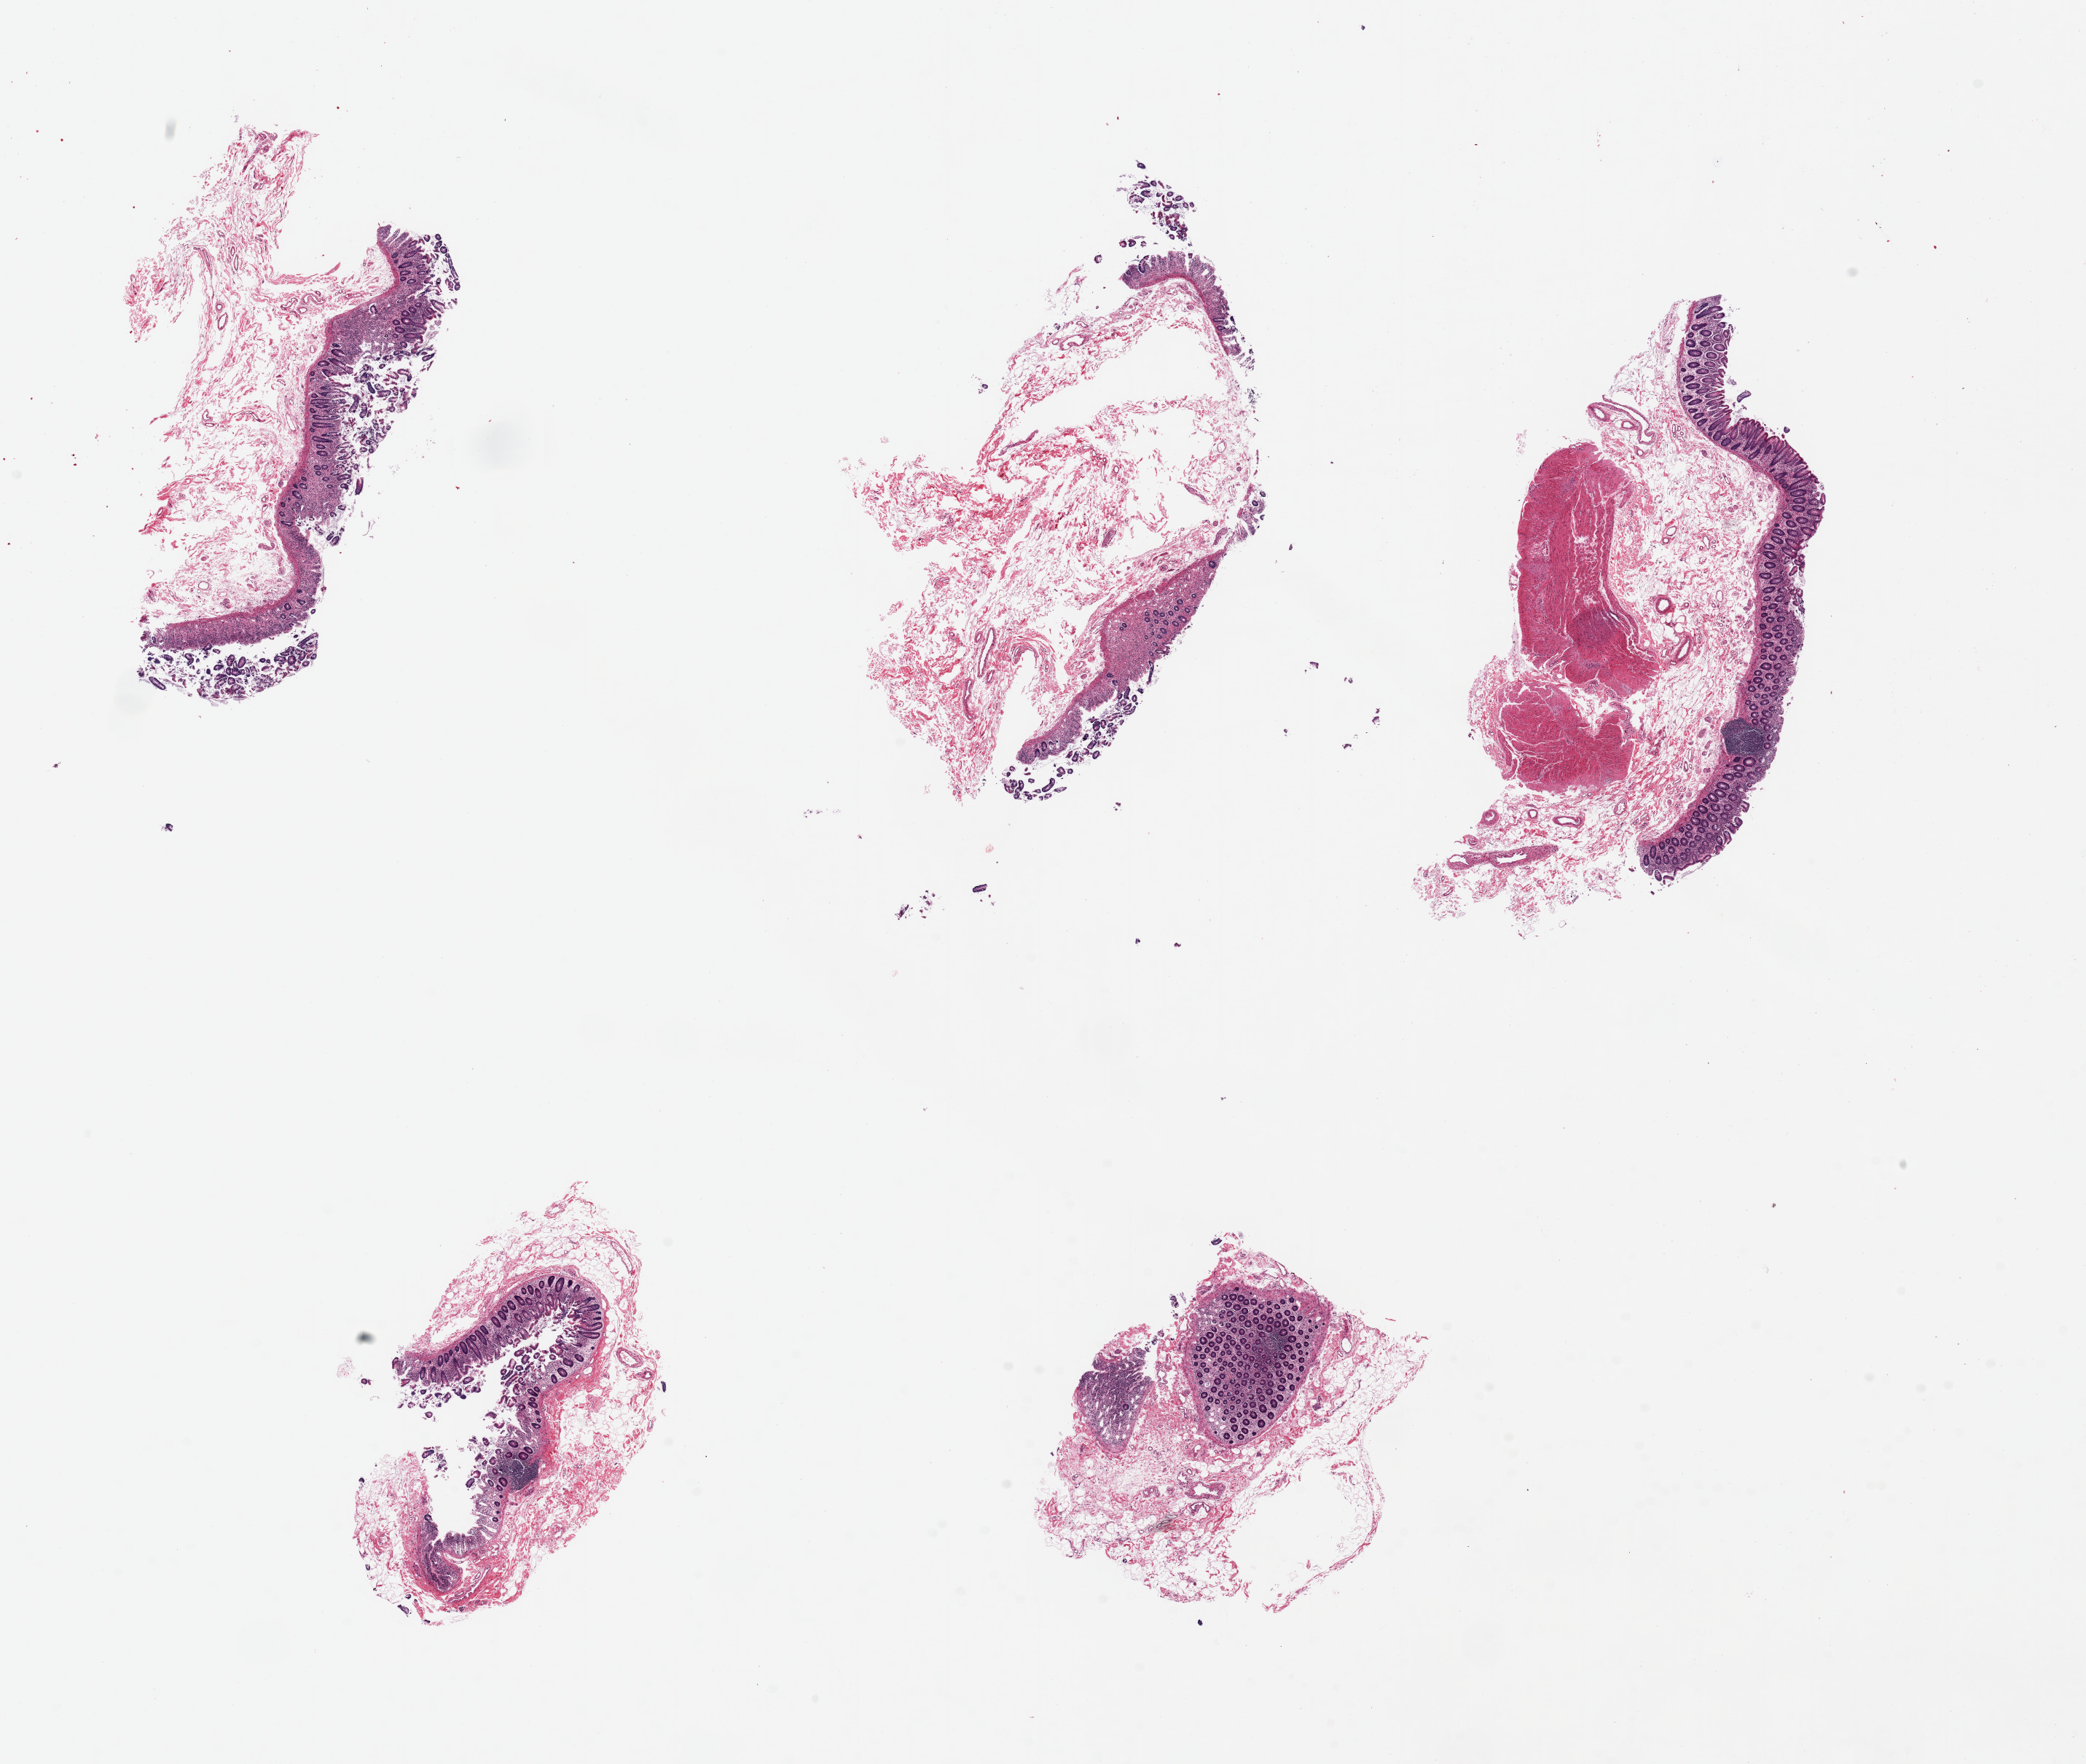
Whole-slide image, H&E stain, brightfield — whole scanned area (about 22.6 x 19.1 mm) shown as a low-resolution overview; PAXgene-fixed paraffin-embedded (PFPE) section; section of transverse colon (target tissue); tissue donor sample.
Review note (as recorded): 6 pieces ~6x2.5mm, 10% mucosa, relatively well preserved.